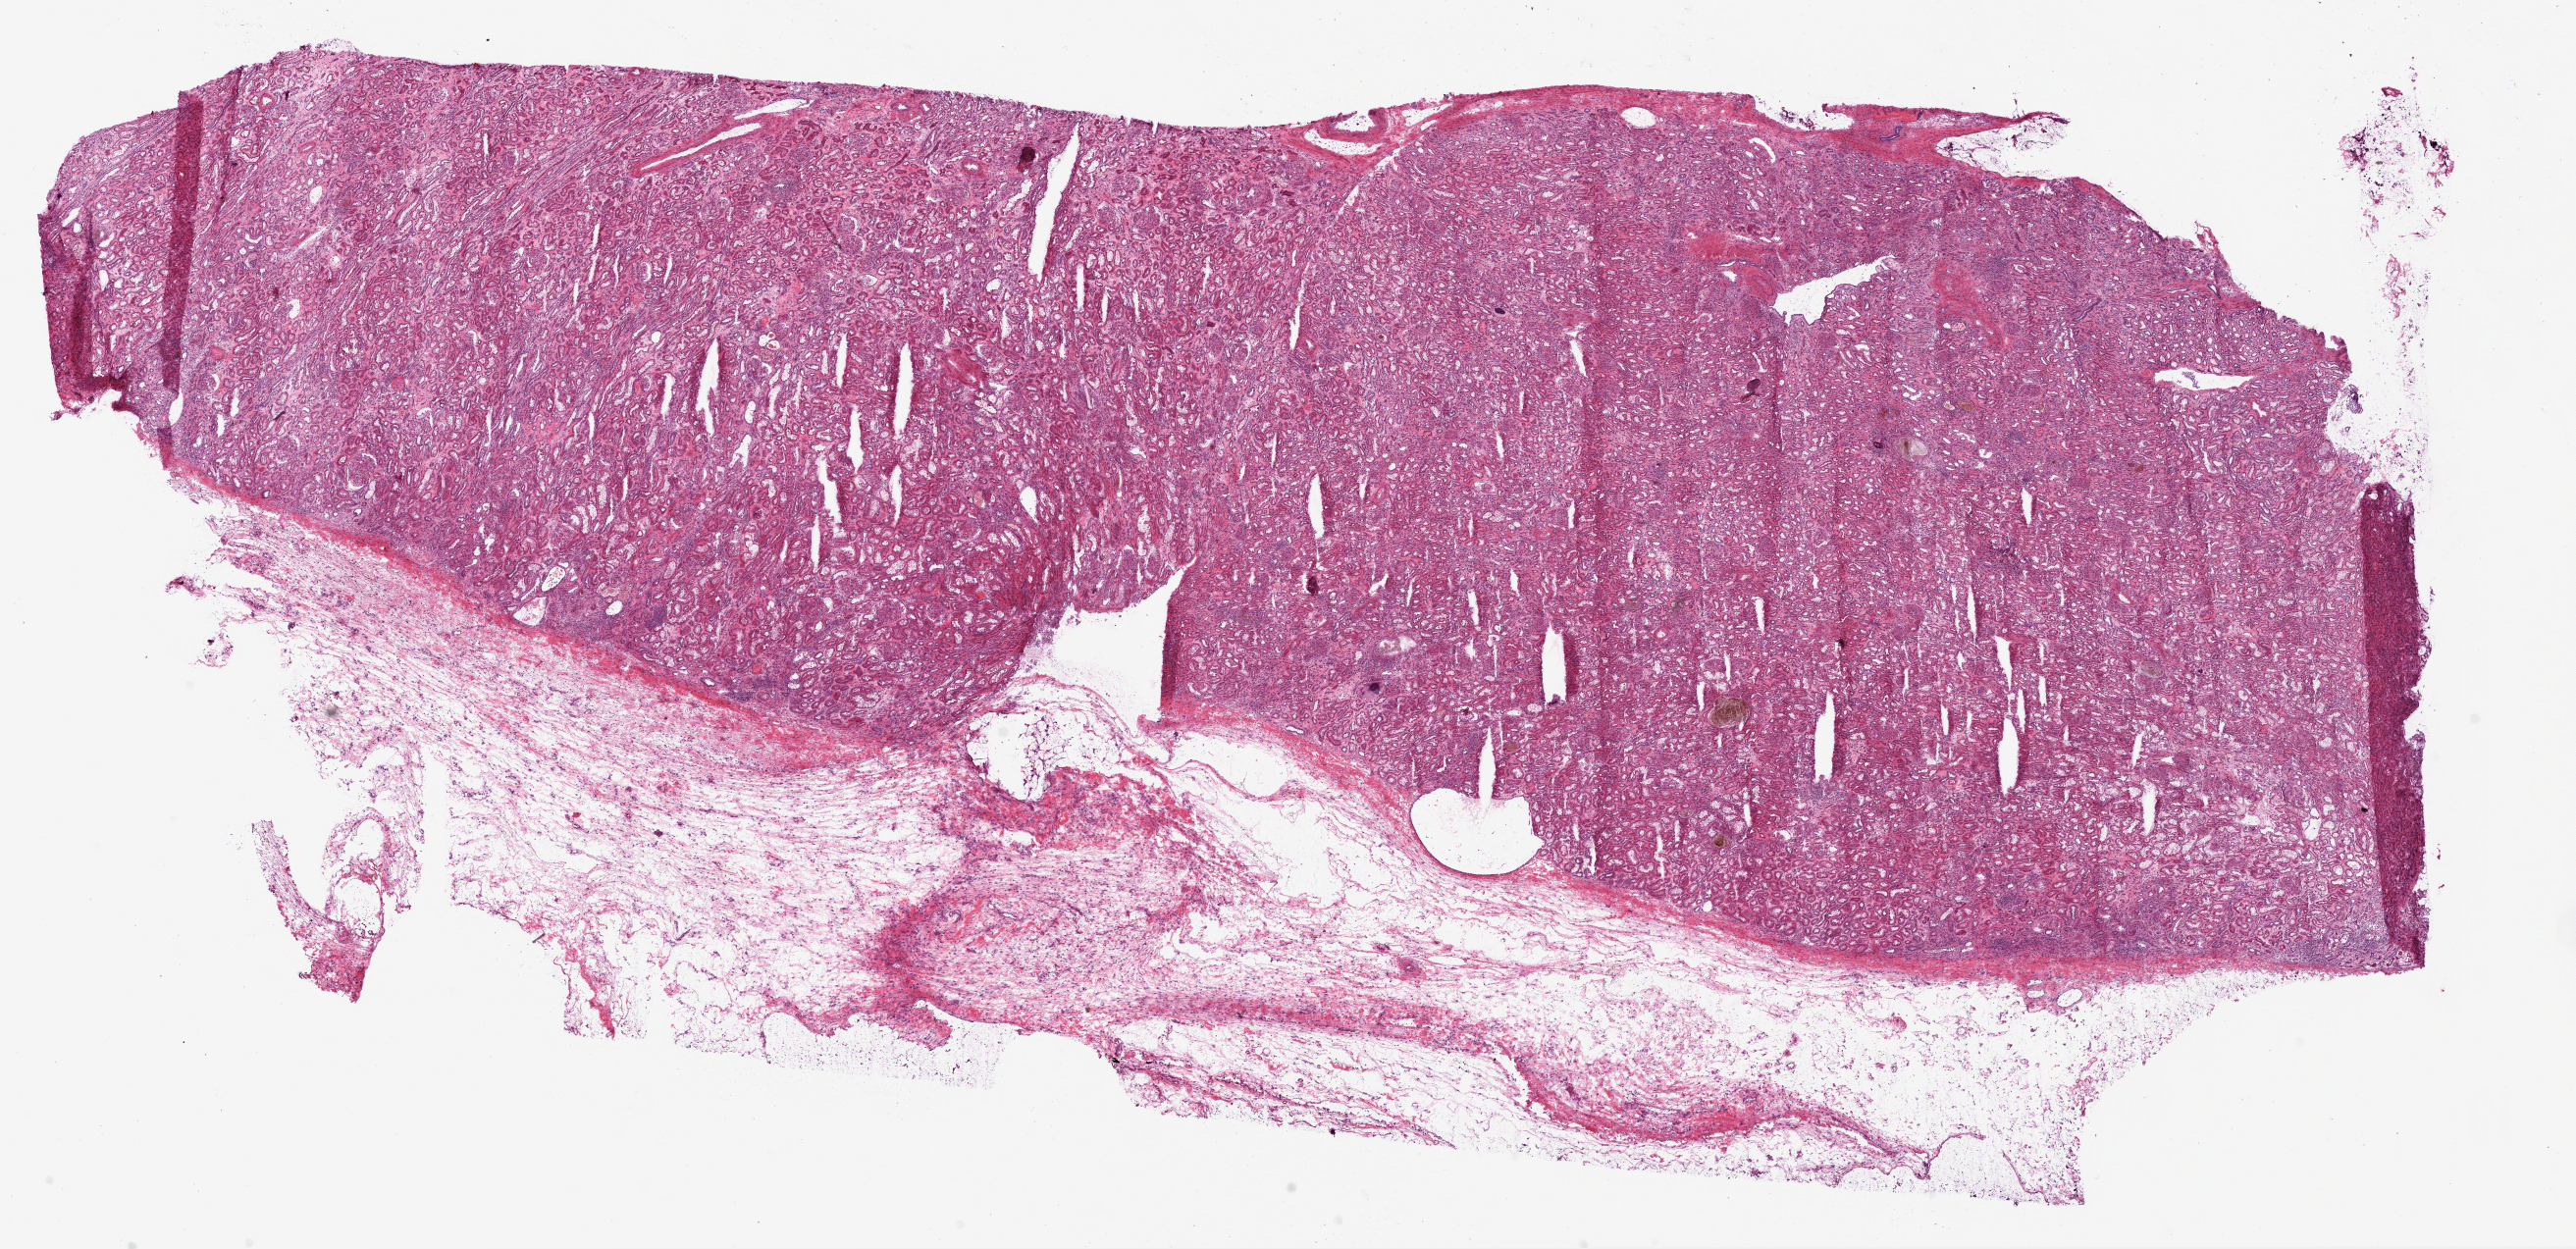
Whole-slide histology image, Hematoxylin and eosin (H&E) stained — shown as a low-resolution overview of the whole scanned area (about 21.1 x 10.2 mm, acquisition: 20x scan); frozen section from the bottom of the tissue portion; sample: solid tissue normal (non-tumour tissue), kidney. Male, age 75 years at initial diagnosis.
- this section: solid tissue normal sample (biorepository sample class)
- patient diagnosis: Papillary adenocarcinoma, NOS